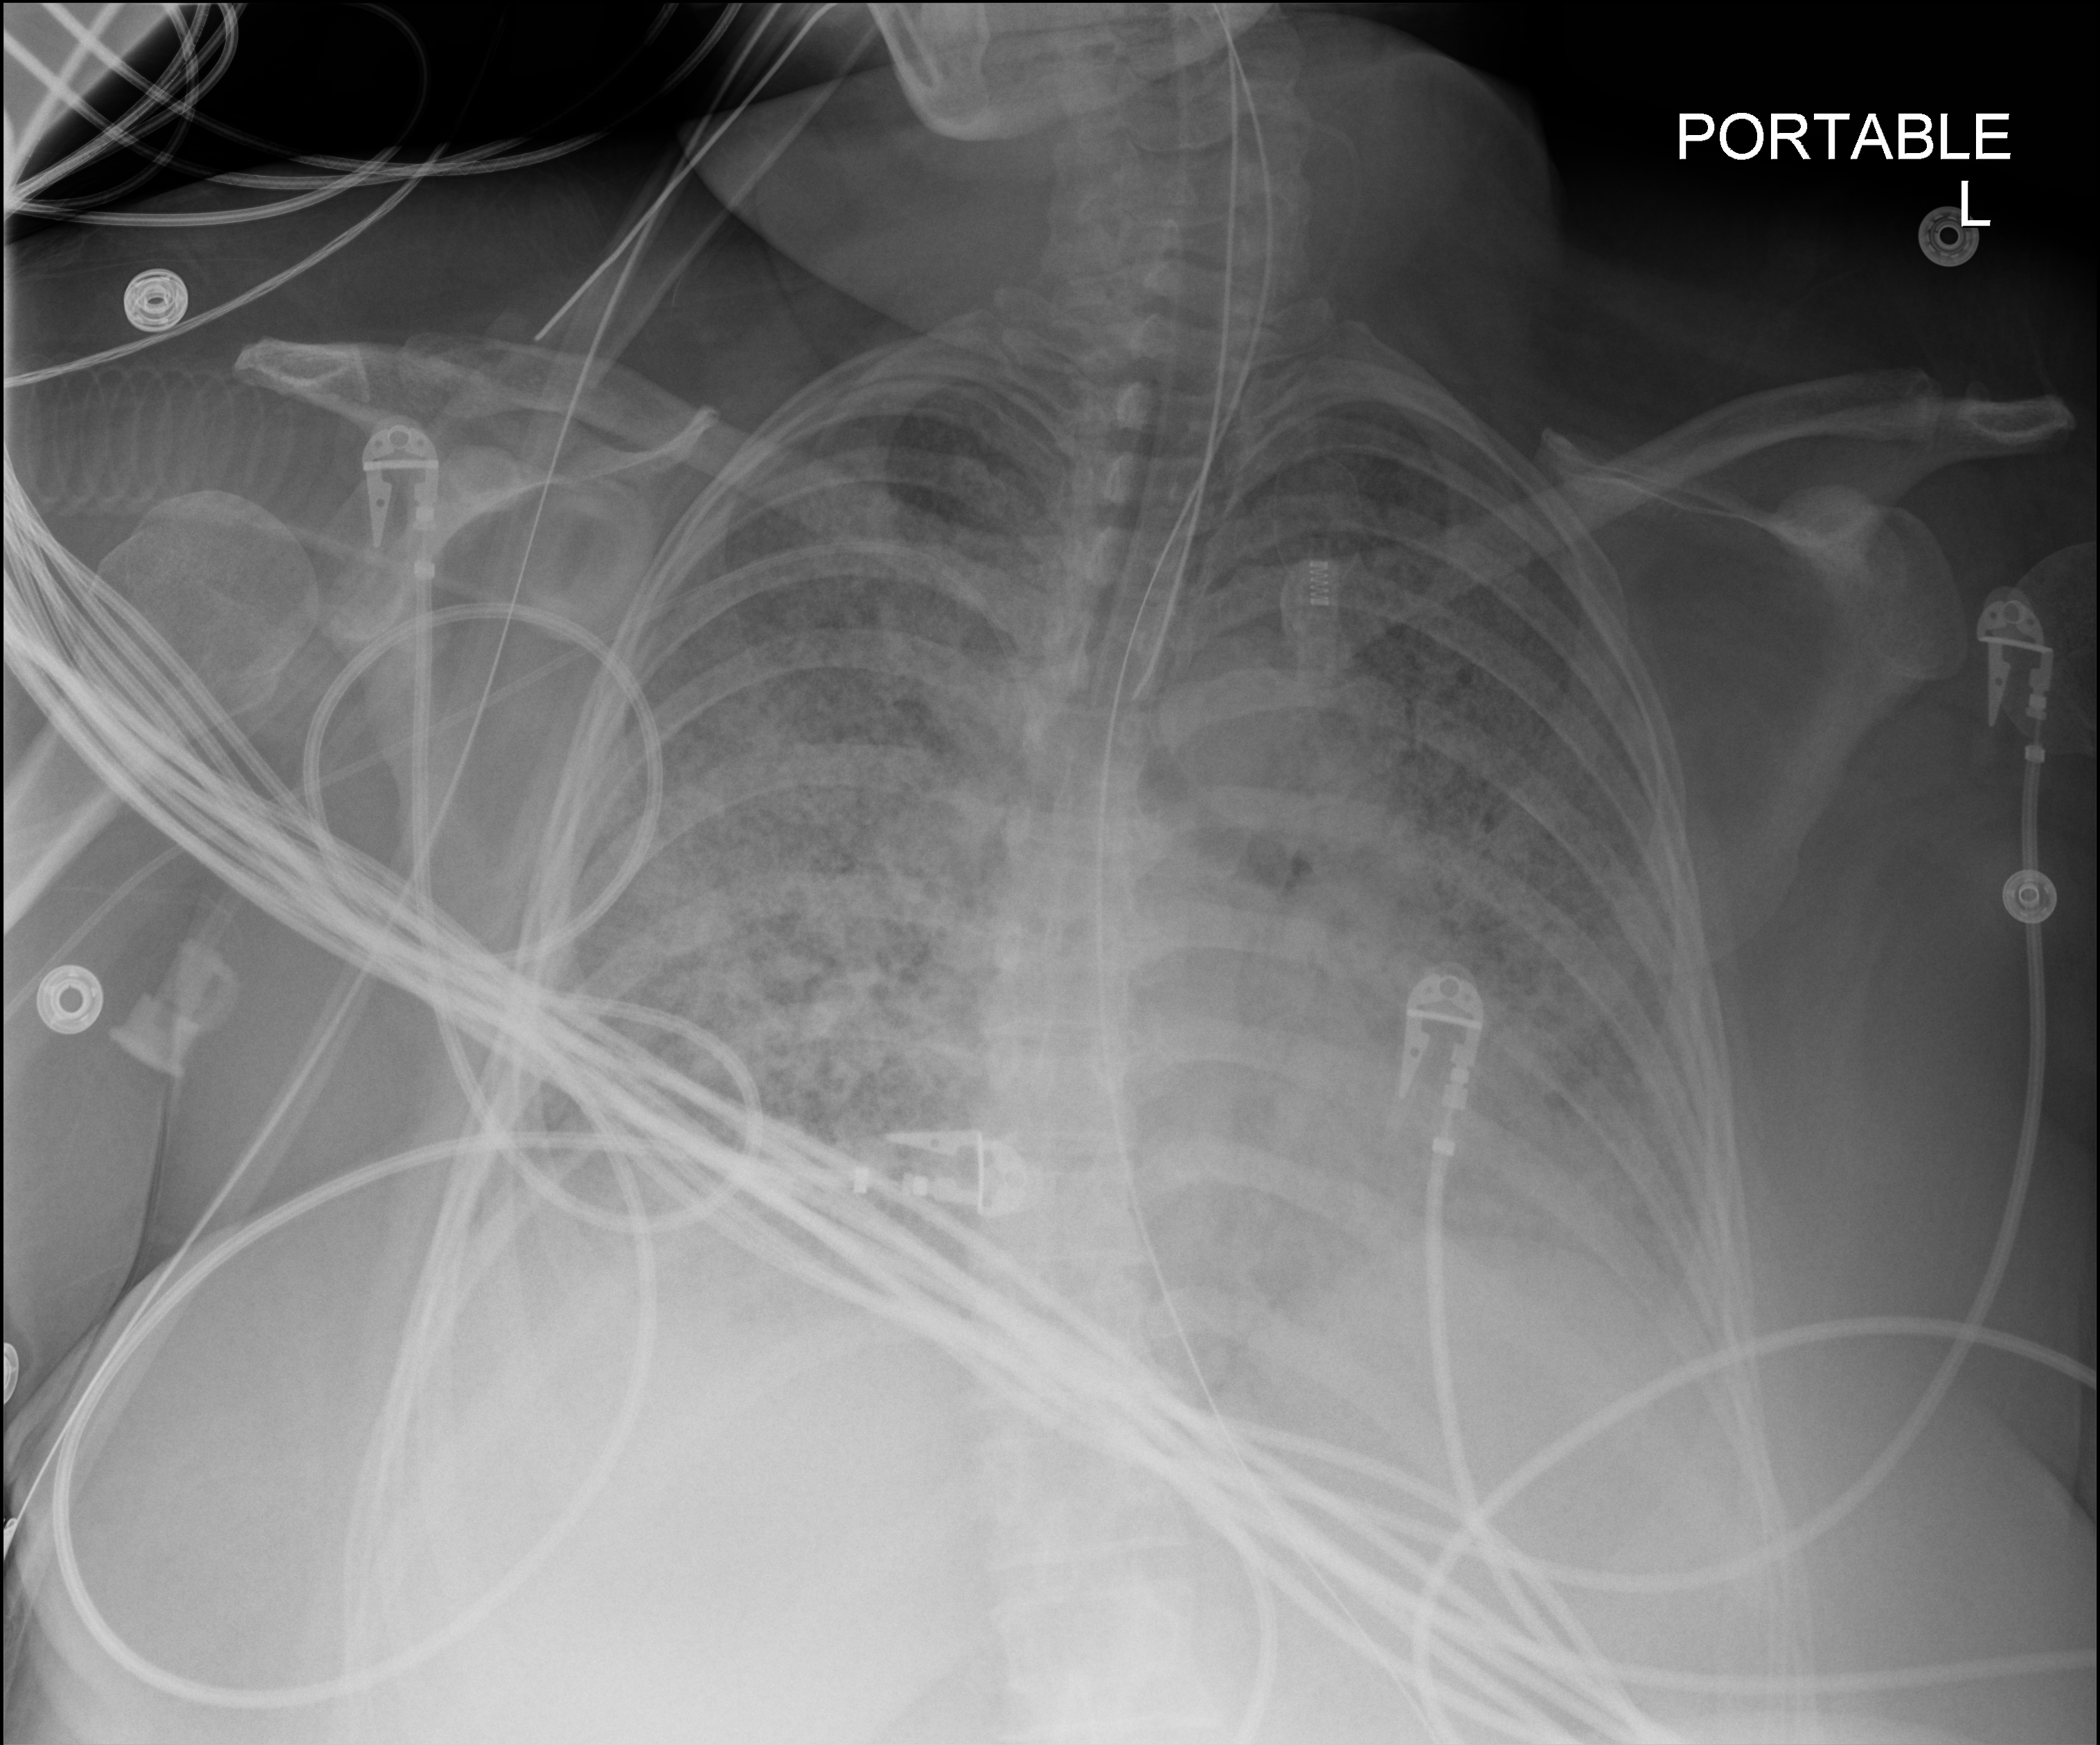
Portable chest radiograph; anteroposterior (AP) projection. Patient hospitalised with COVID-19; female, aged 18–59 years.
Hospital-stay facts (about this admission, not read from this image; timing relative to this image not recorded): other chronic lung disease (admission record): no.